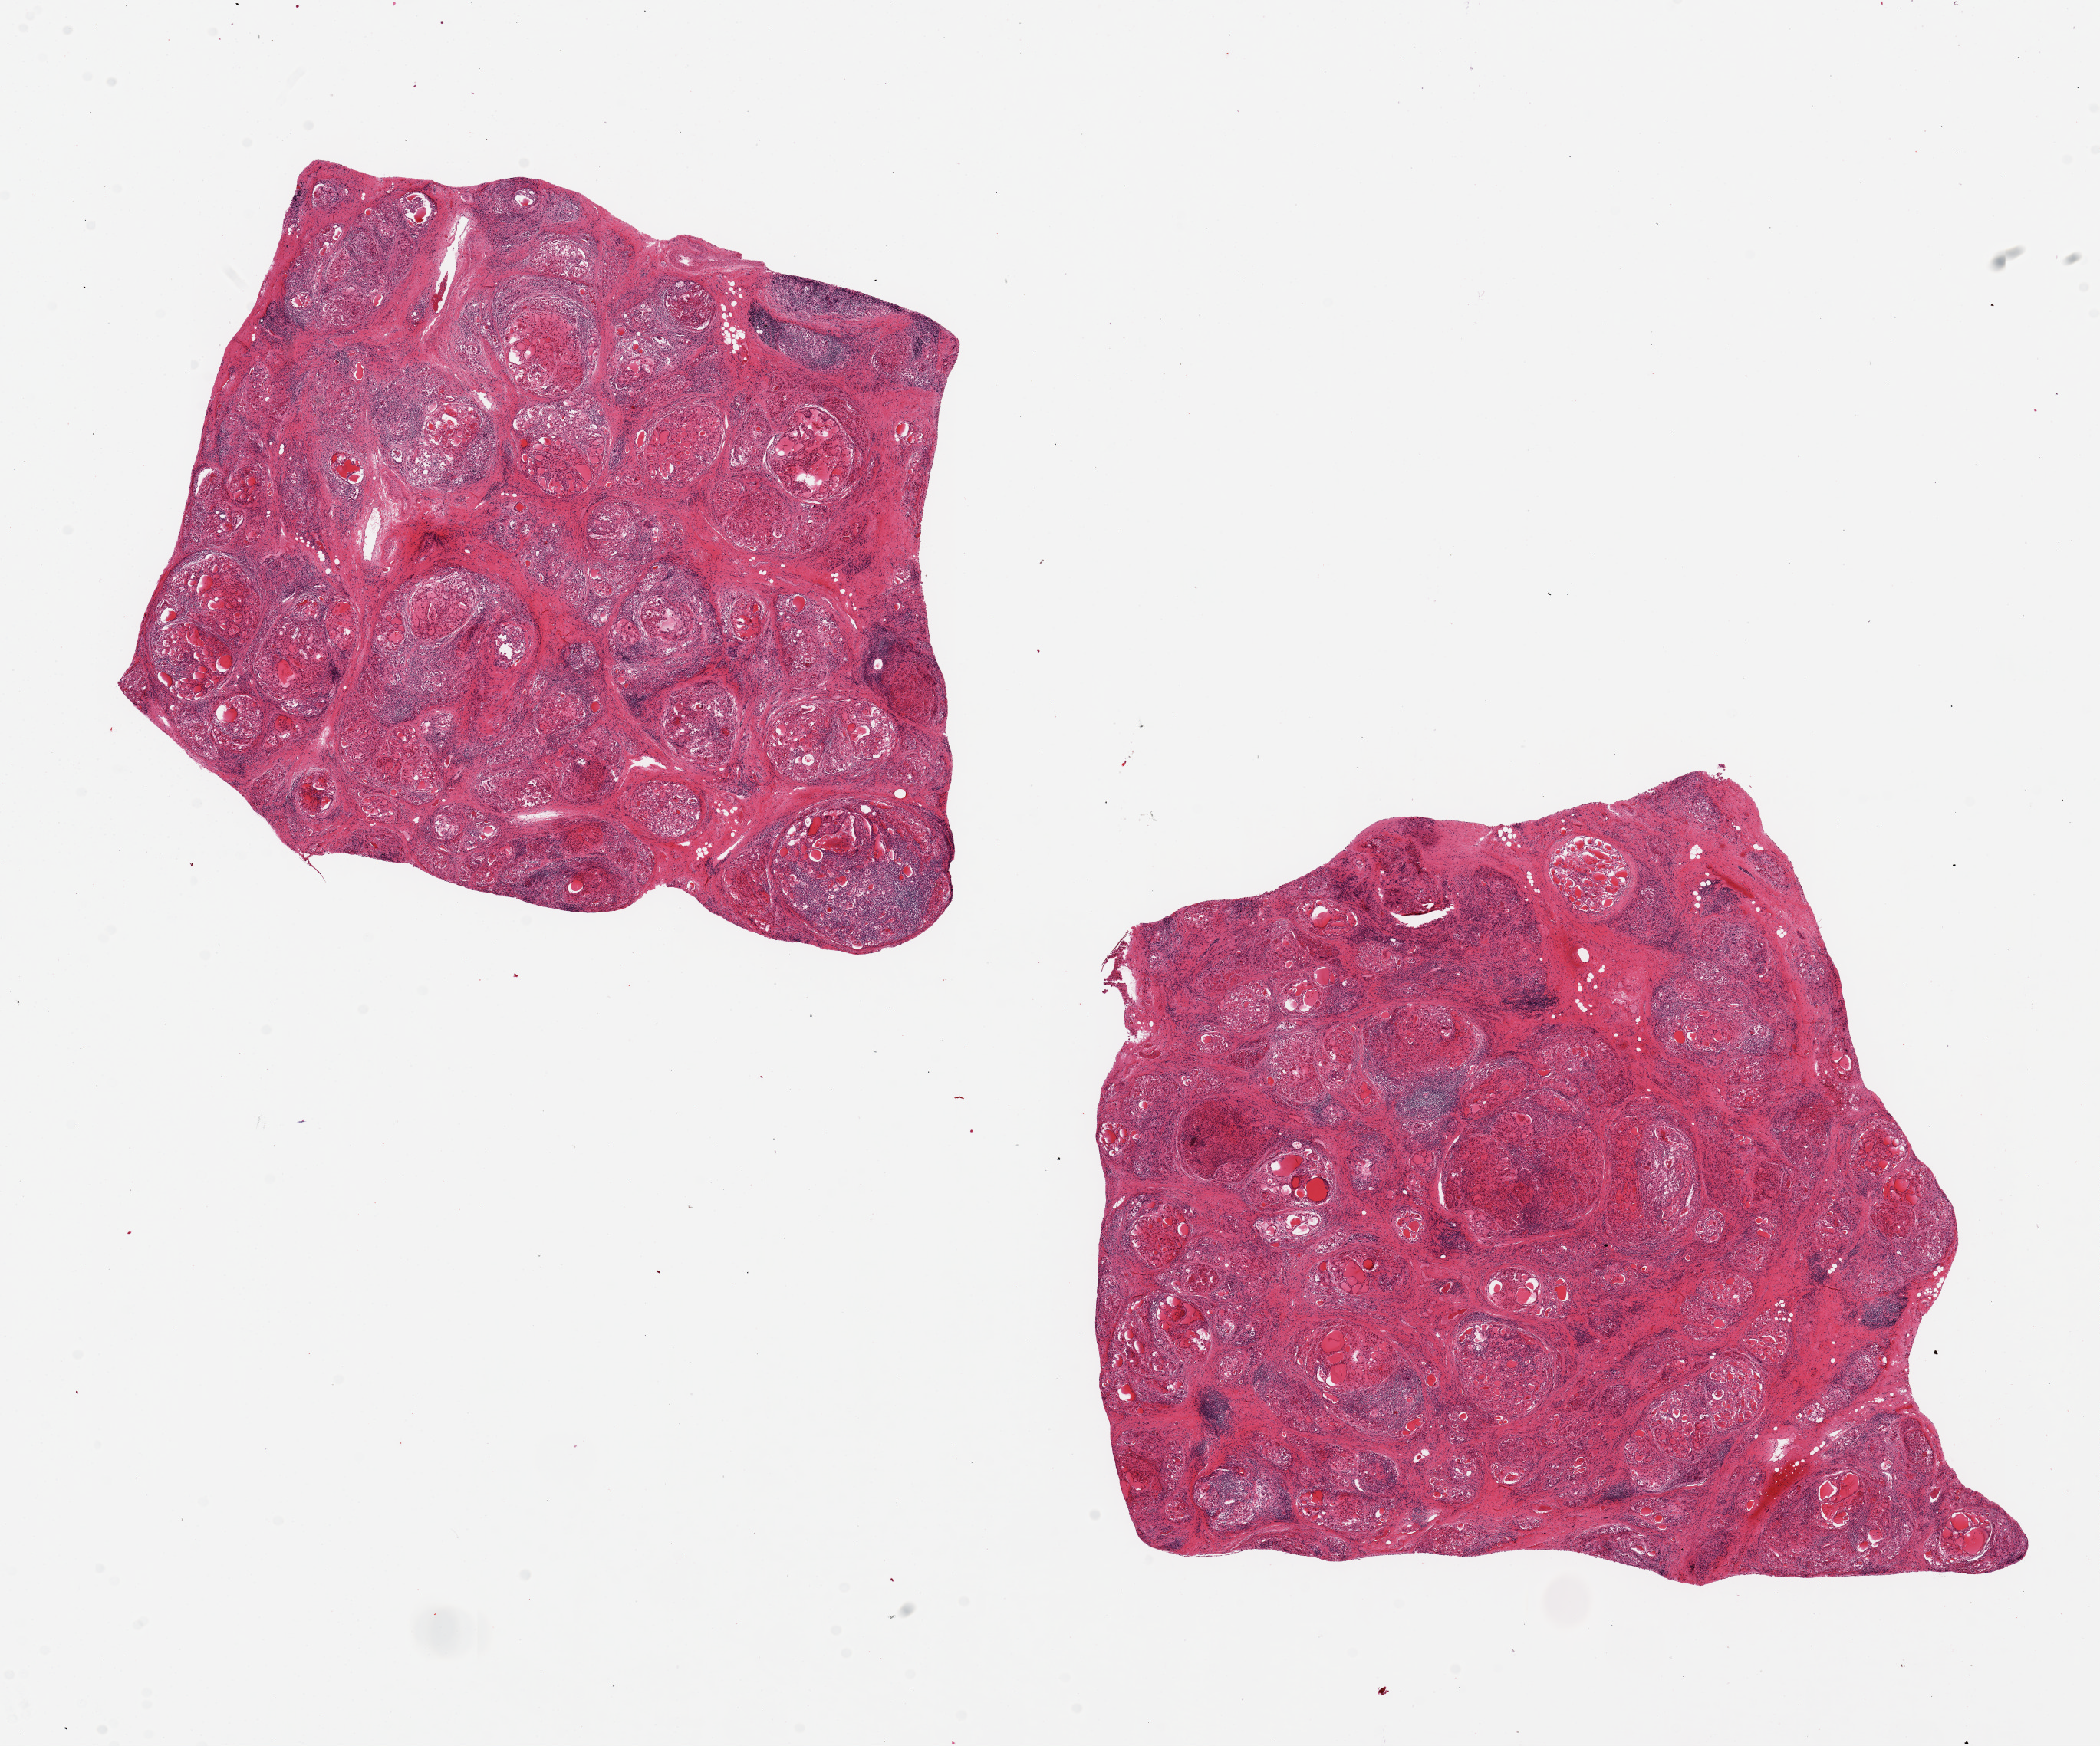
H&E whole-slide image, low-resolution overview of the scanned area, about 21.7 x 18.0 mm, PAXgene-fixed, paraffin-embedded tissue, section of thyroid (target tissue), donor tissue sample.
* review note (as recorded): 2 pieces, 9x7.5 & 9x9mm; extensive fibrosis and lymphoid infiltrate typical of advanced Hashimoto thyoiditis (correlates with patient's hypothyroidism); oxyphilic metaplasia